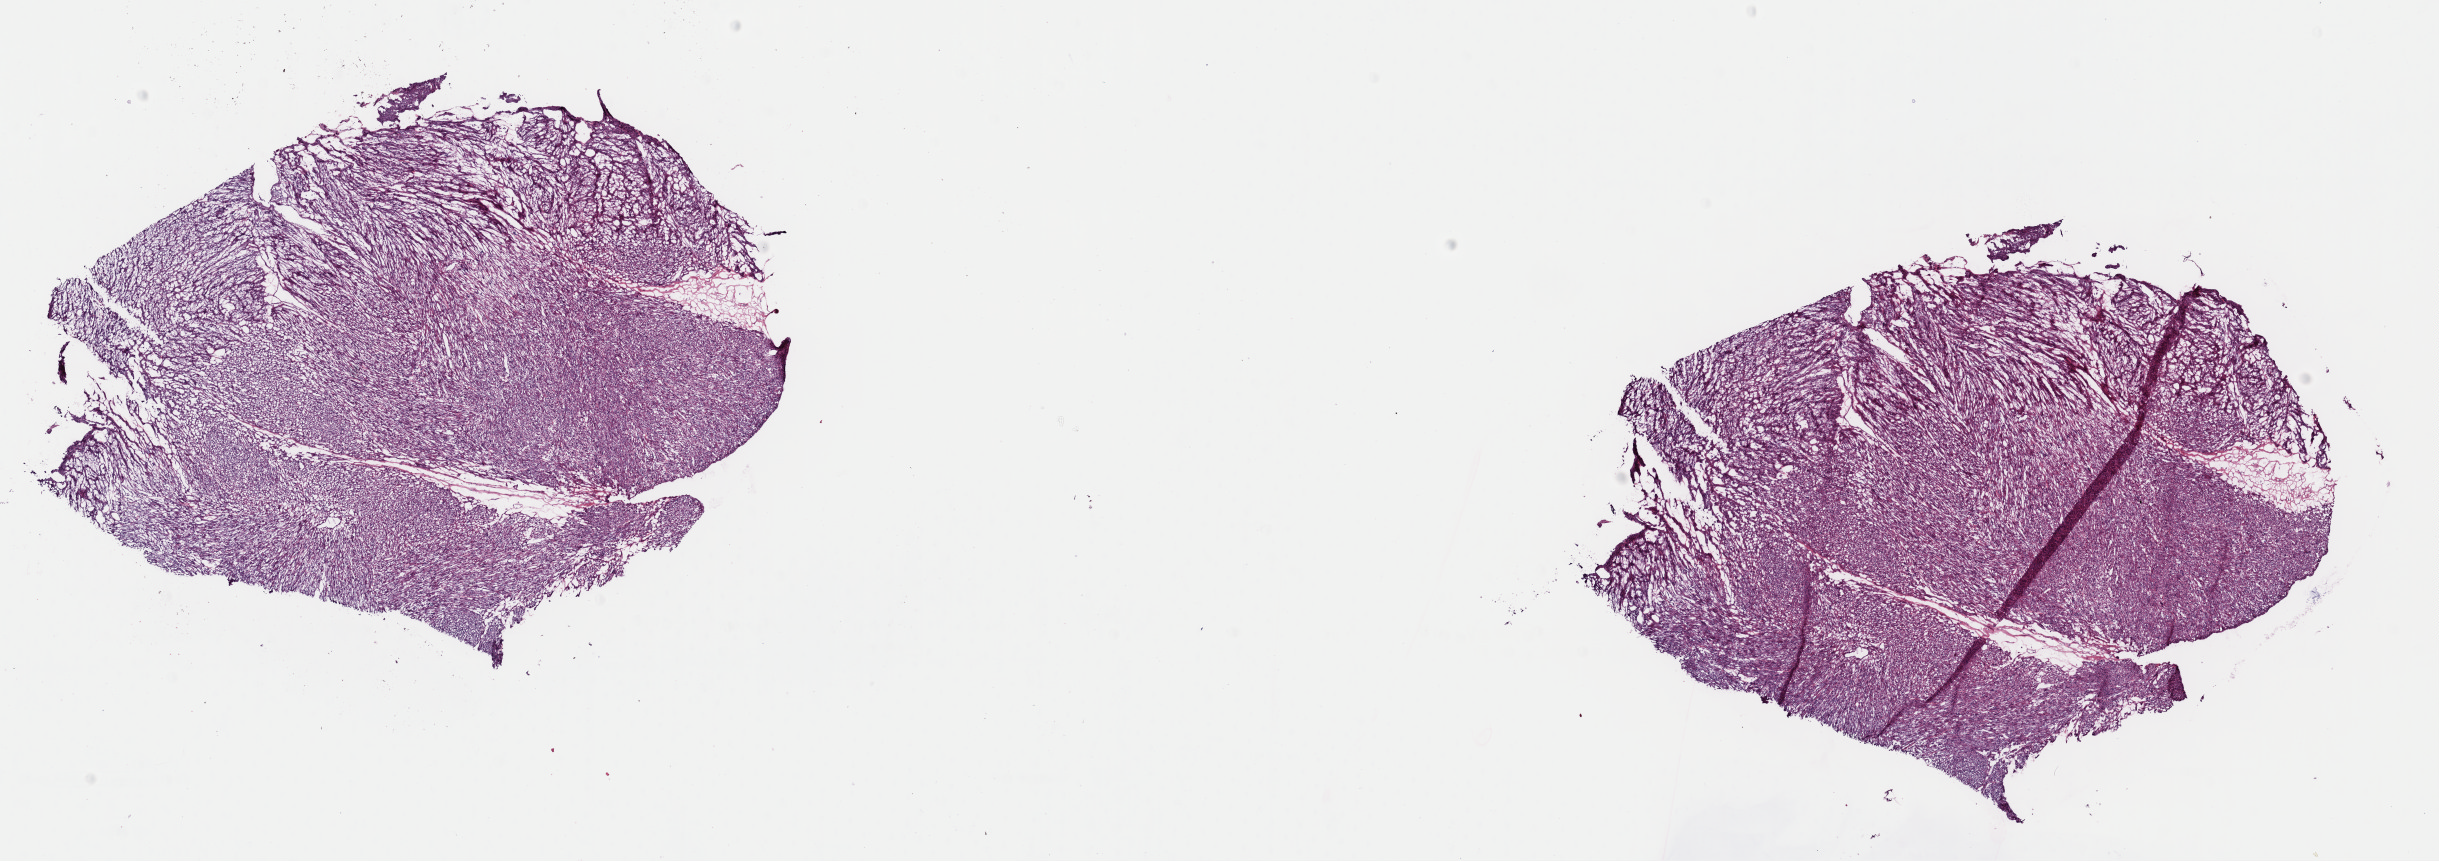
H&E whole-slide image — shown as a low-resolution overview of the whole scanned area (about 19.3 x 6.8 mm, acquisition: 40x scan); frozen section; primary tumour sample from the retroperitoneum and peritoneum. Female patient; age at initial diagnosis 63 years. Pathologist review of this section (percent, as recorded): tumour cells 80%, tumour nuclei 80%, normal cells 0%, stromal cells 20%, necrosis 0%. Inflammatory infiltration, as recorded: lymphocyte infiltration 2%, monocyte infiltration 1%, neutrophil infiltration 0%.
Histologic diagnosis: Leiomyosarcoma, NOS (retroperitoneum).